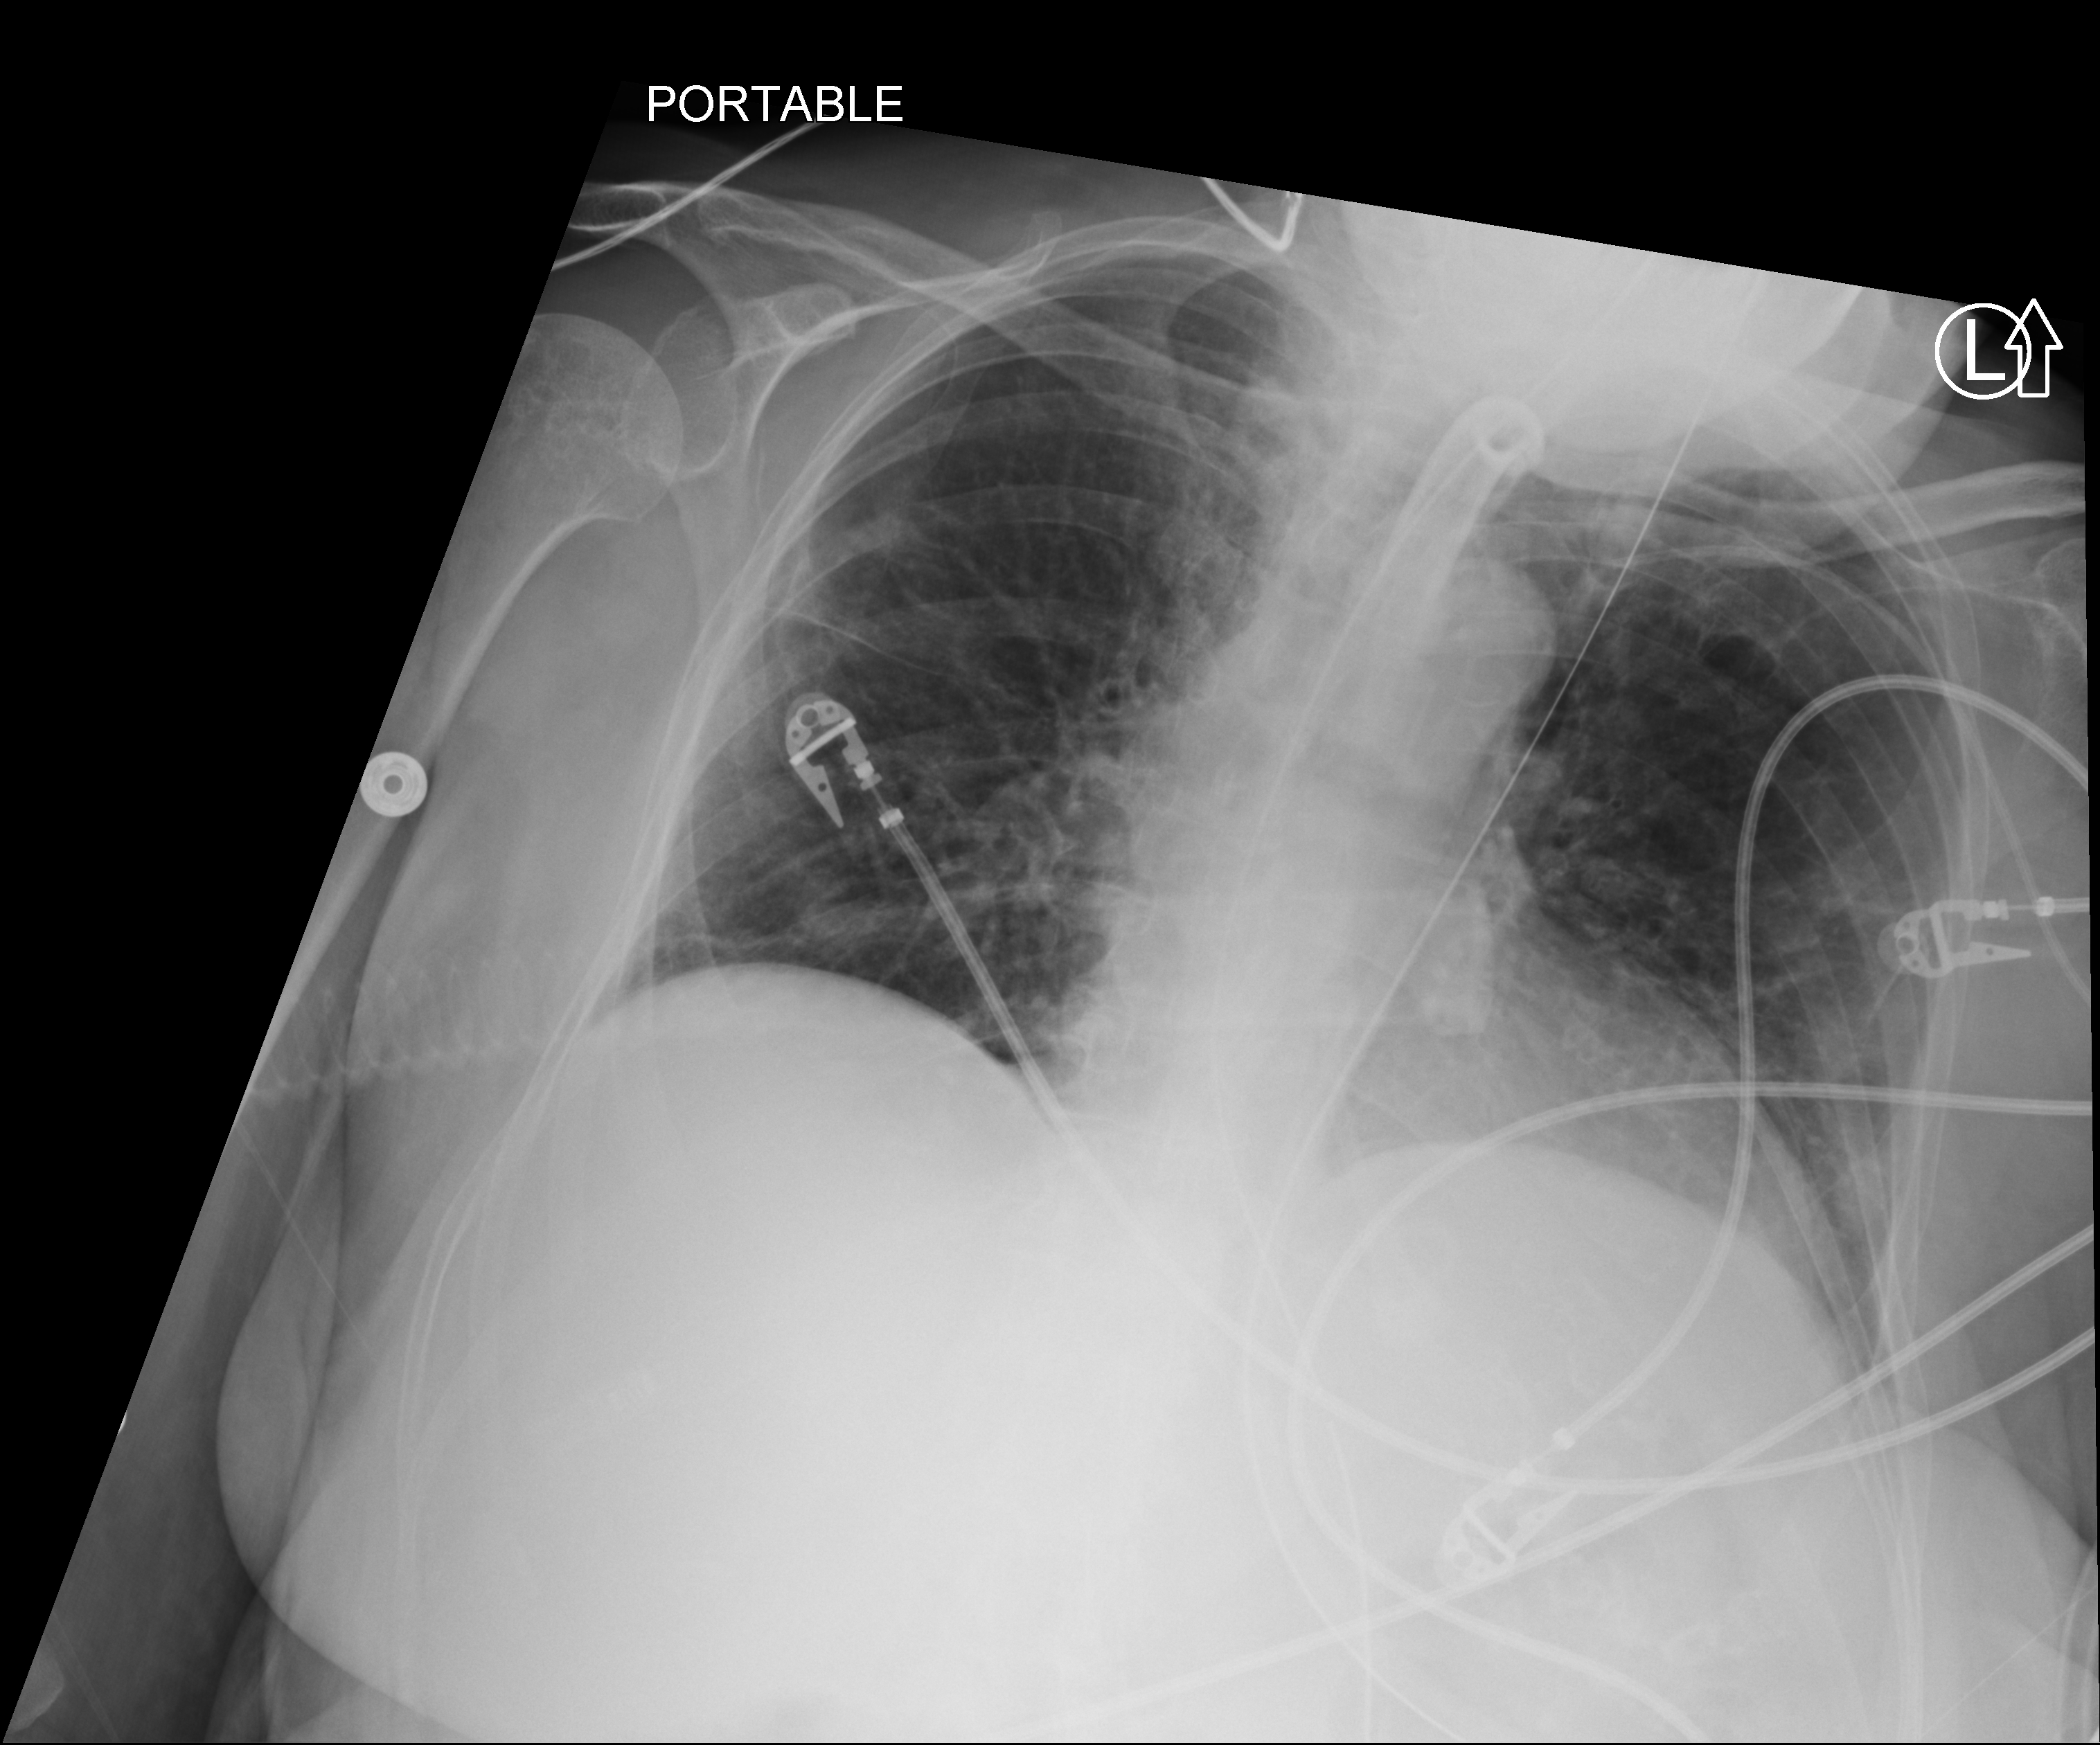
Bedside chest radiograph (computed radiography), anteroposterior (AP) projection. Patient hospitalised with COVID-19; female, aged 75–90 years.
Hospital-stay facts (about this admission, not read from this image; timing relative to this image not recorded):
- mechanically ventilated during this hospital stay: yes
- length of hospital stay: 82 days
- diabetes (admission record): no